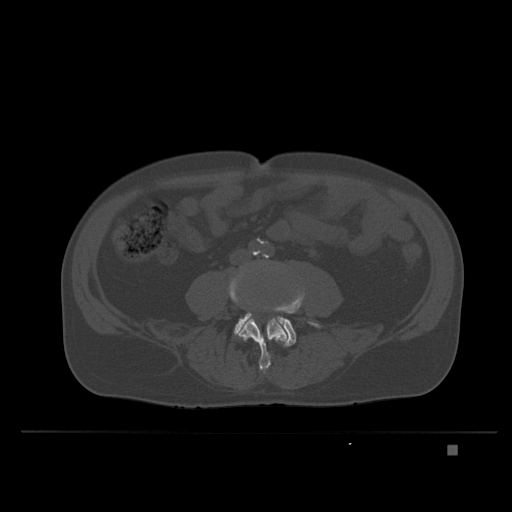
CT including the spine, one axial slice. Bone window (W 1800 / L 400 HU). 1.5 mm slice thickness. 512 × 512 image matrix, field of view 434 × 434 mm. Male patient, age 73 years. Case-level facts recorded for this patient, not image findings: primary cancer: skin.
Structures marked on this image (semi-automatic segmentation, software-assisted and operator-edited):
- L4 vertebra: box from (x=228, y=267) to (x=288, y=374) px
- L5 vertebra: (x=234, y=293)–(x=320, y=347)